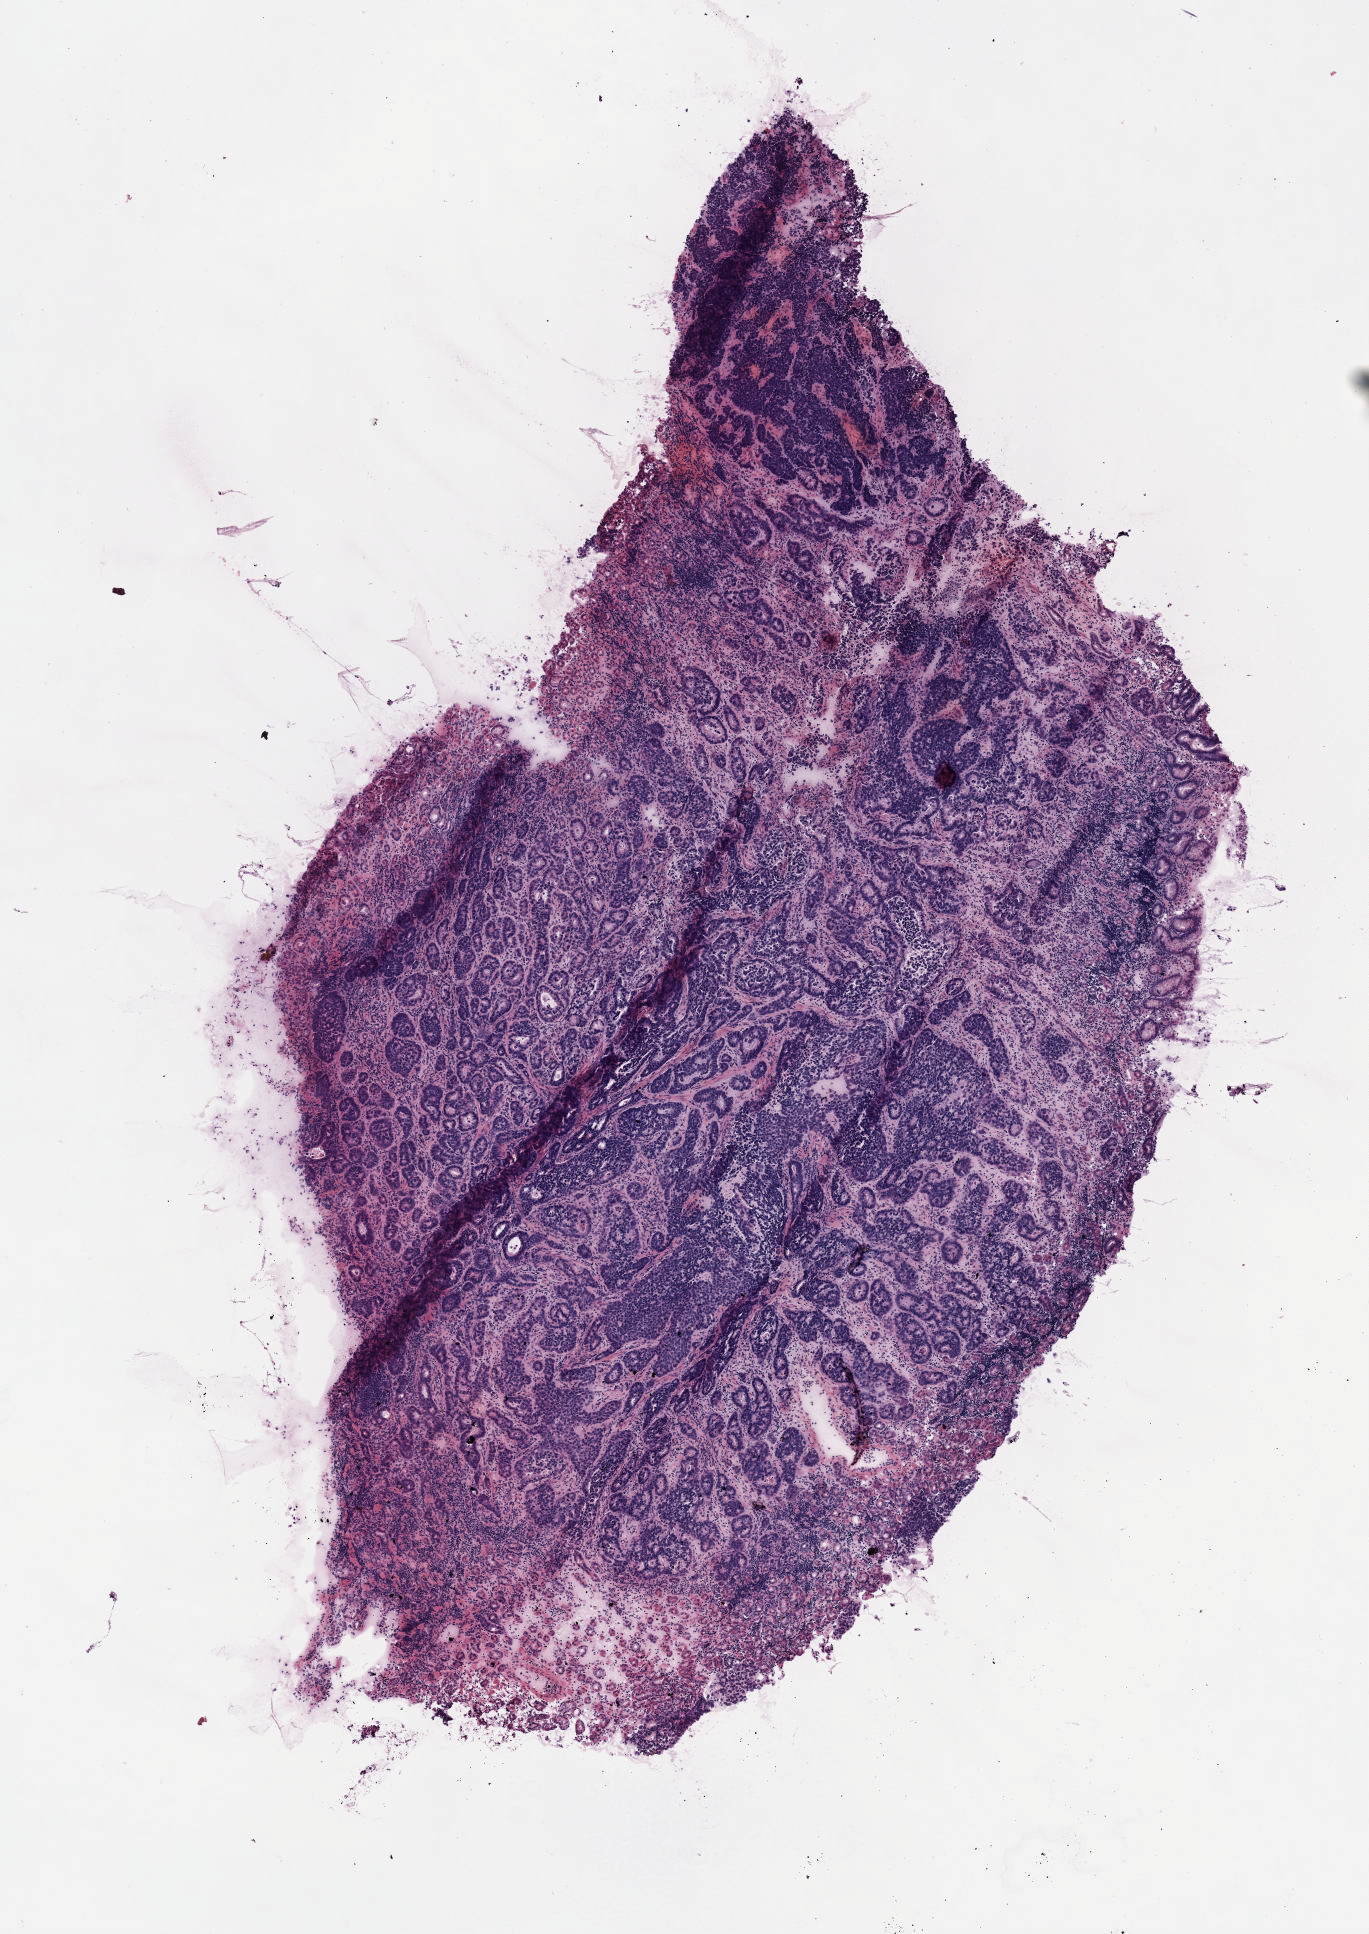
Digitized H&E tissue section (whole slide), shown as a low-resolution overview of the whole scanned area (about 5.5 x 7.8 mm), frozen section from the top of the tissue portion, sample: primary tumour, esophagus. Male, age 66 years at initial diagnosis. Histologic grade: G2 (moderately differentiated). Pathologist review of this section (percent, as recorded): tumour cells 60%, tumour nuclei 70%, normal cells 0%, stromal cells 40%, necrosis 0%. Infiltration values recorded for this section: lymphocyte infiltration 0%, monocyte infiltration 0%, neutrophil infiltration 0%.
Pathologic diagnosis: Adenocarcinoma, NOS (lower third of esophagus). AJCC pathologic stage: III (5th edition). Lymph nodes positive (case pathology): 4 of 19 examined.